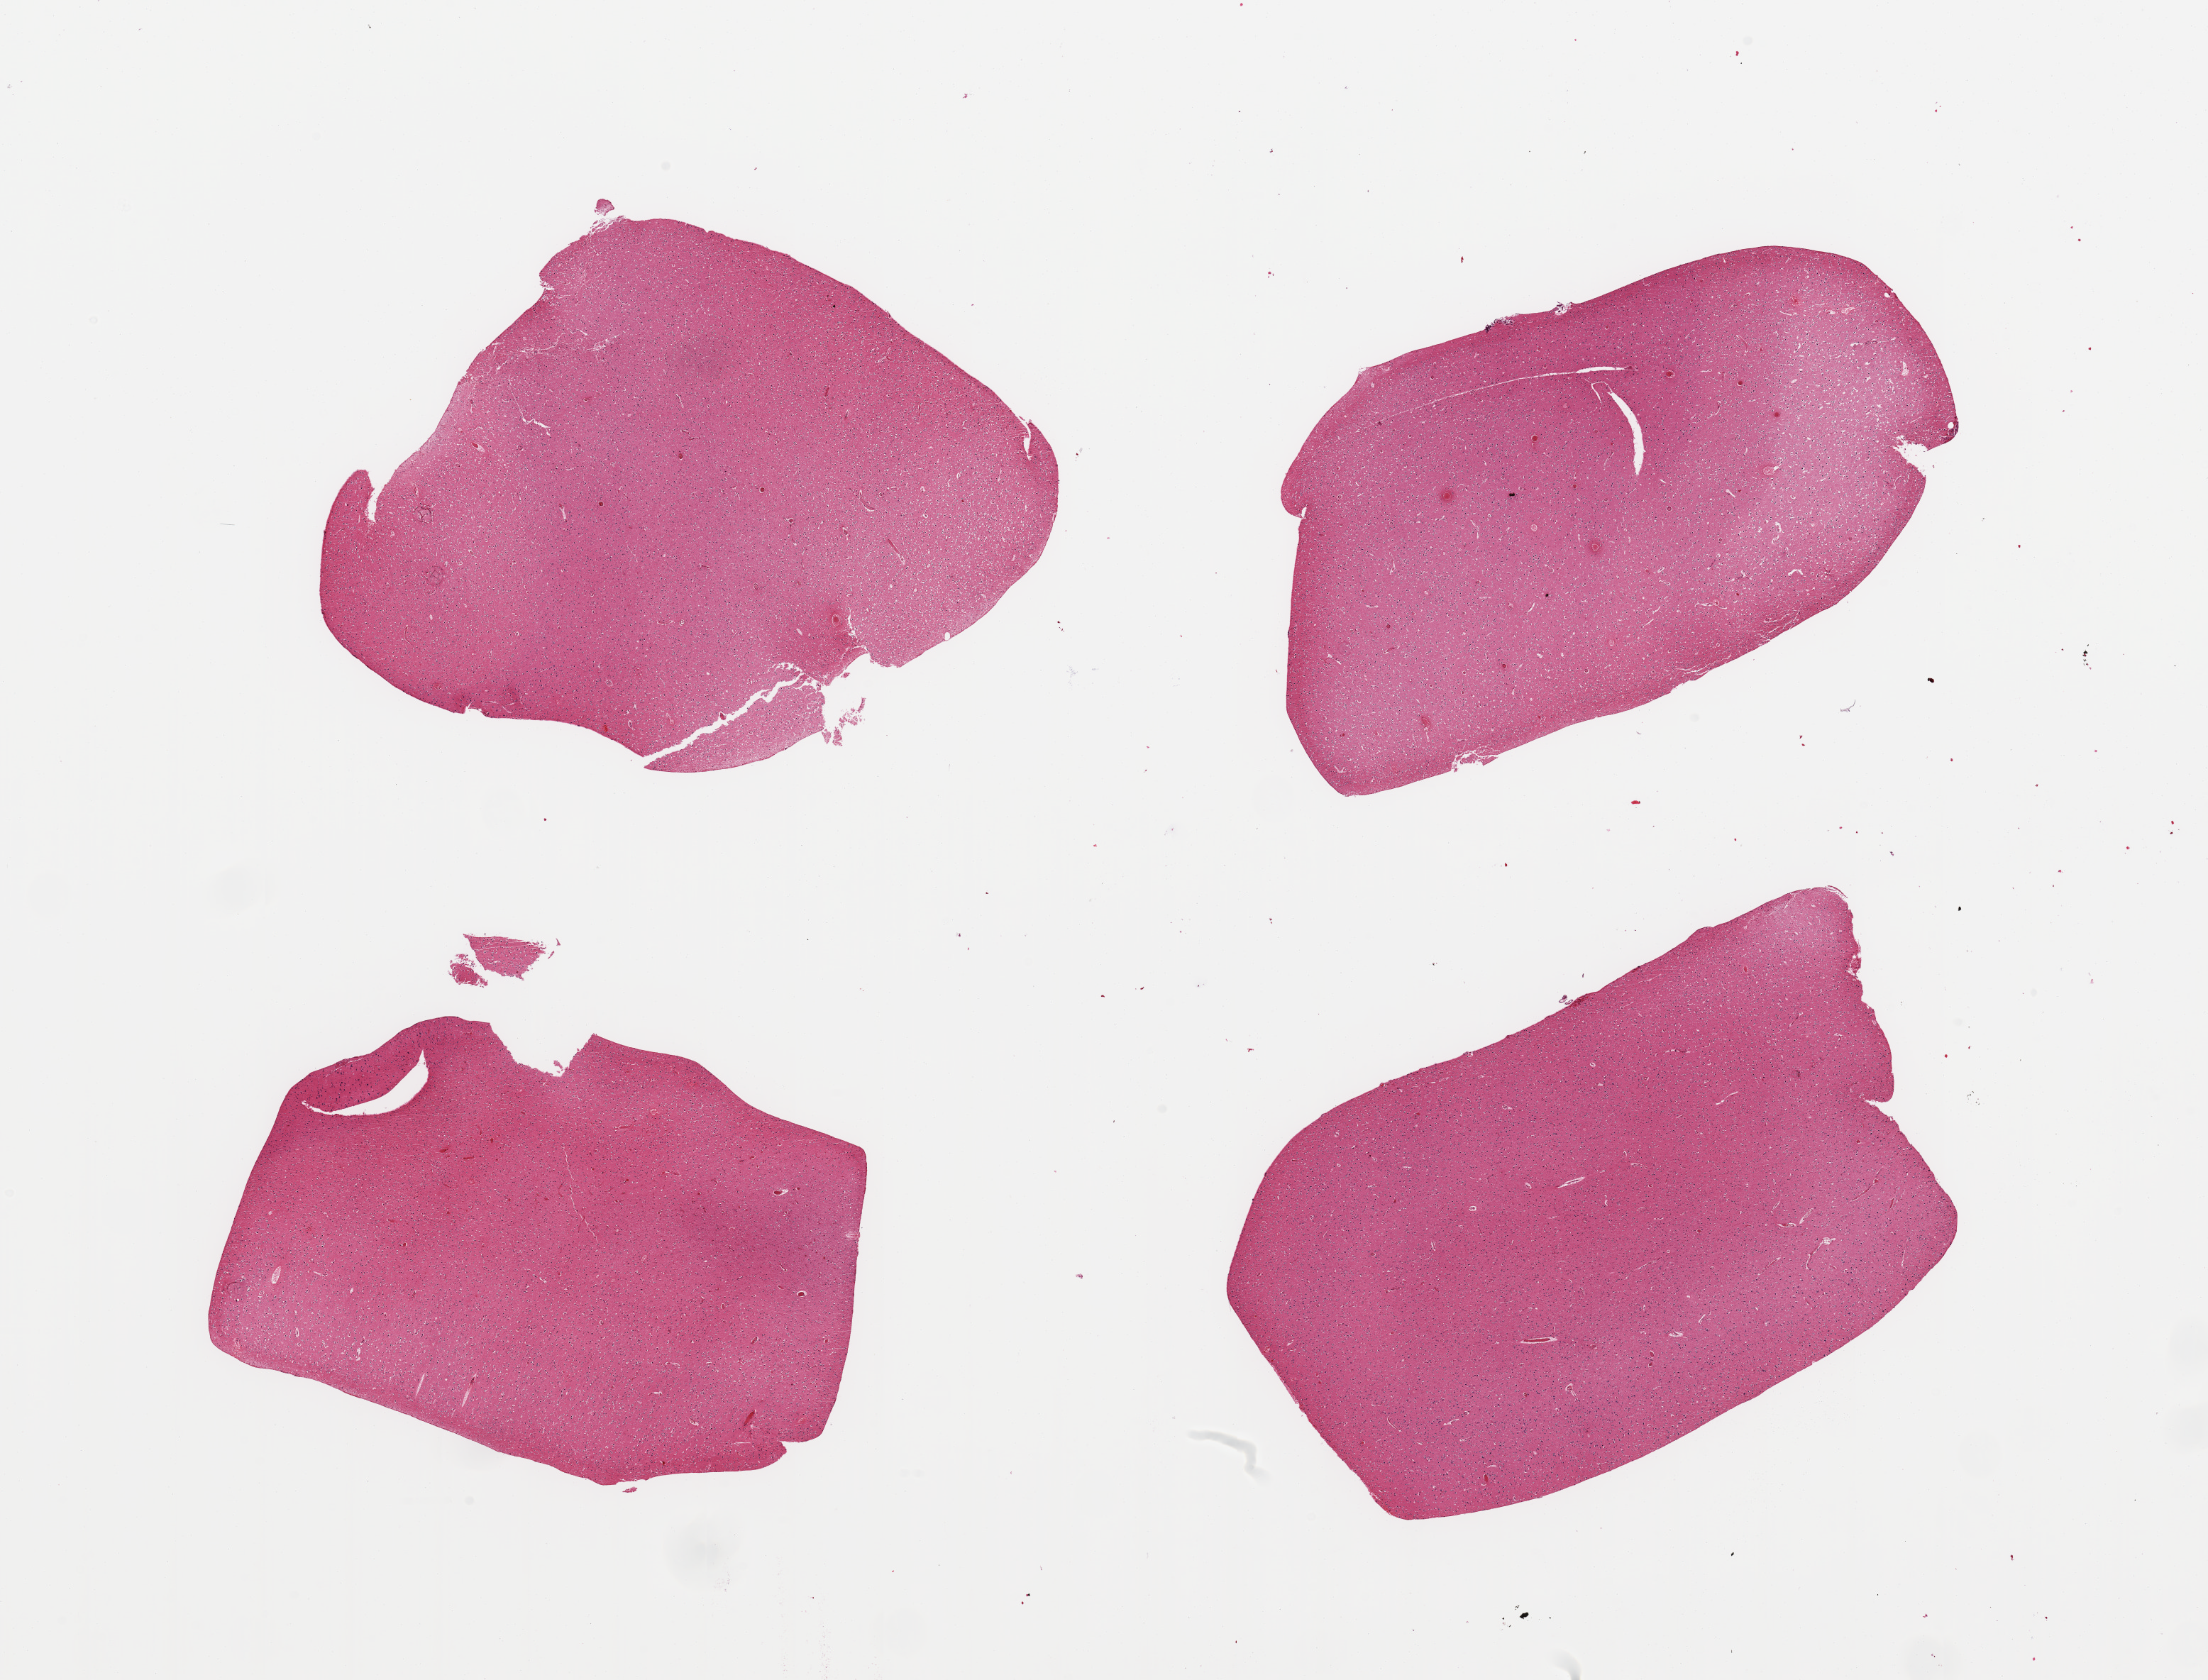
Whole-slide image, H&E stain — shown as a low-resolution overview of the whole scanned area (about 24.6 x 18.7 mm, from a 20x scan); PAXgene-fixed, paraffin-embedded tissue; target tissue: cerebral cortex; donor tissue sample.
* pathologist's review note for this sample: 4 pieces, no abnormalities